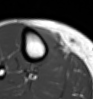
MRI of an extremity soft-tissue mass, one axial slice. Position 23 of 54 along the scan axis. MR volume resampled by the dataset authors to the PET/CT grid (not the native acquisition matrix). 3.27 mm slice thickness. 93 × 99 image matrix, field of view 91 × 97 mm. Female patient. Case-level facts recorded for this patient, not image findings: histological type: undifferentiated – high grade; grade: high; site of the primary tumour: right thigh.
Structures marked on this image (expert contour drawn on MRI and transferred to this co-registered scan by the dataset authors):
- gross tumour volume (mass): bounding box <32,25,64,62> (left, top, right, bottom; pixels)